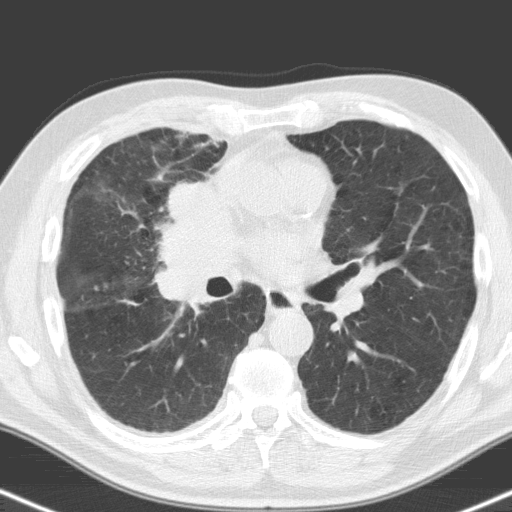
Low-dose screening chest CT, one axial slice; slice 89 of 160 in the series (ordered by position); 120 kVp; lung window (W 1500 / L -600 HU); 512 × 512 image matrix.
Annotated regions visible in this slice (outlined manually by an expert reader):
- lesion 1 (tumor, hilum of right lung): bounding box <159,180,234,305> (left, top, right, bottom; pixels)